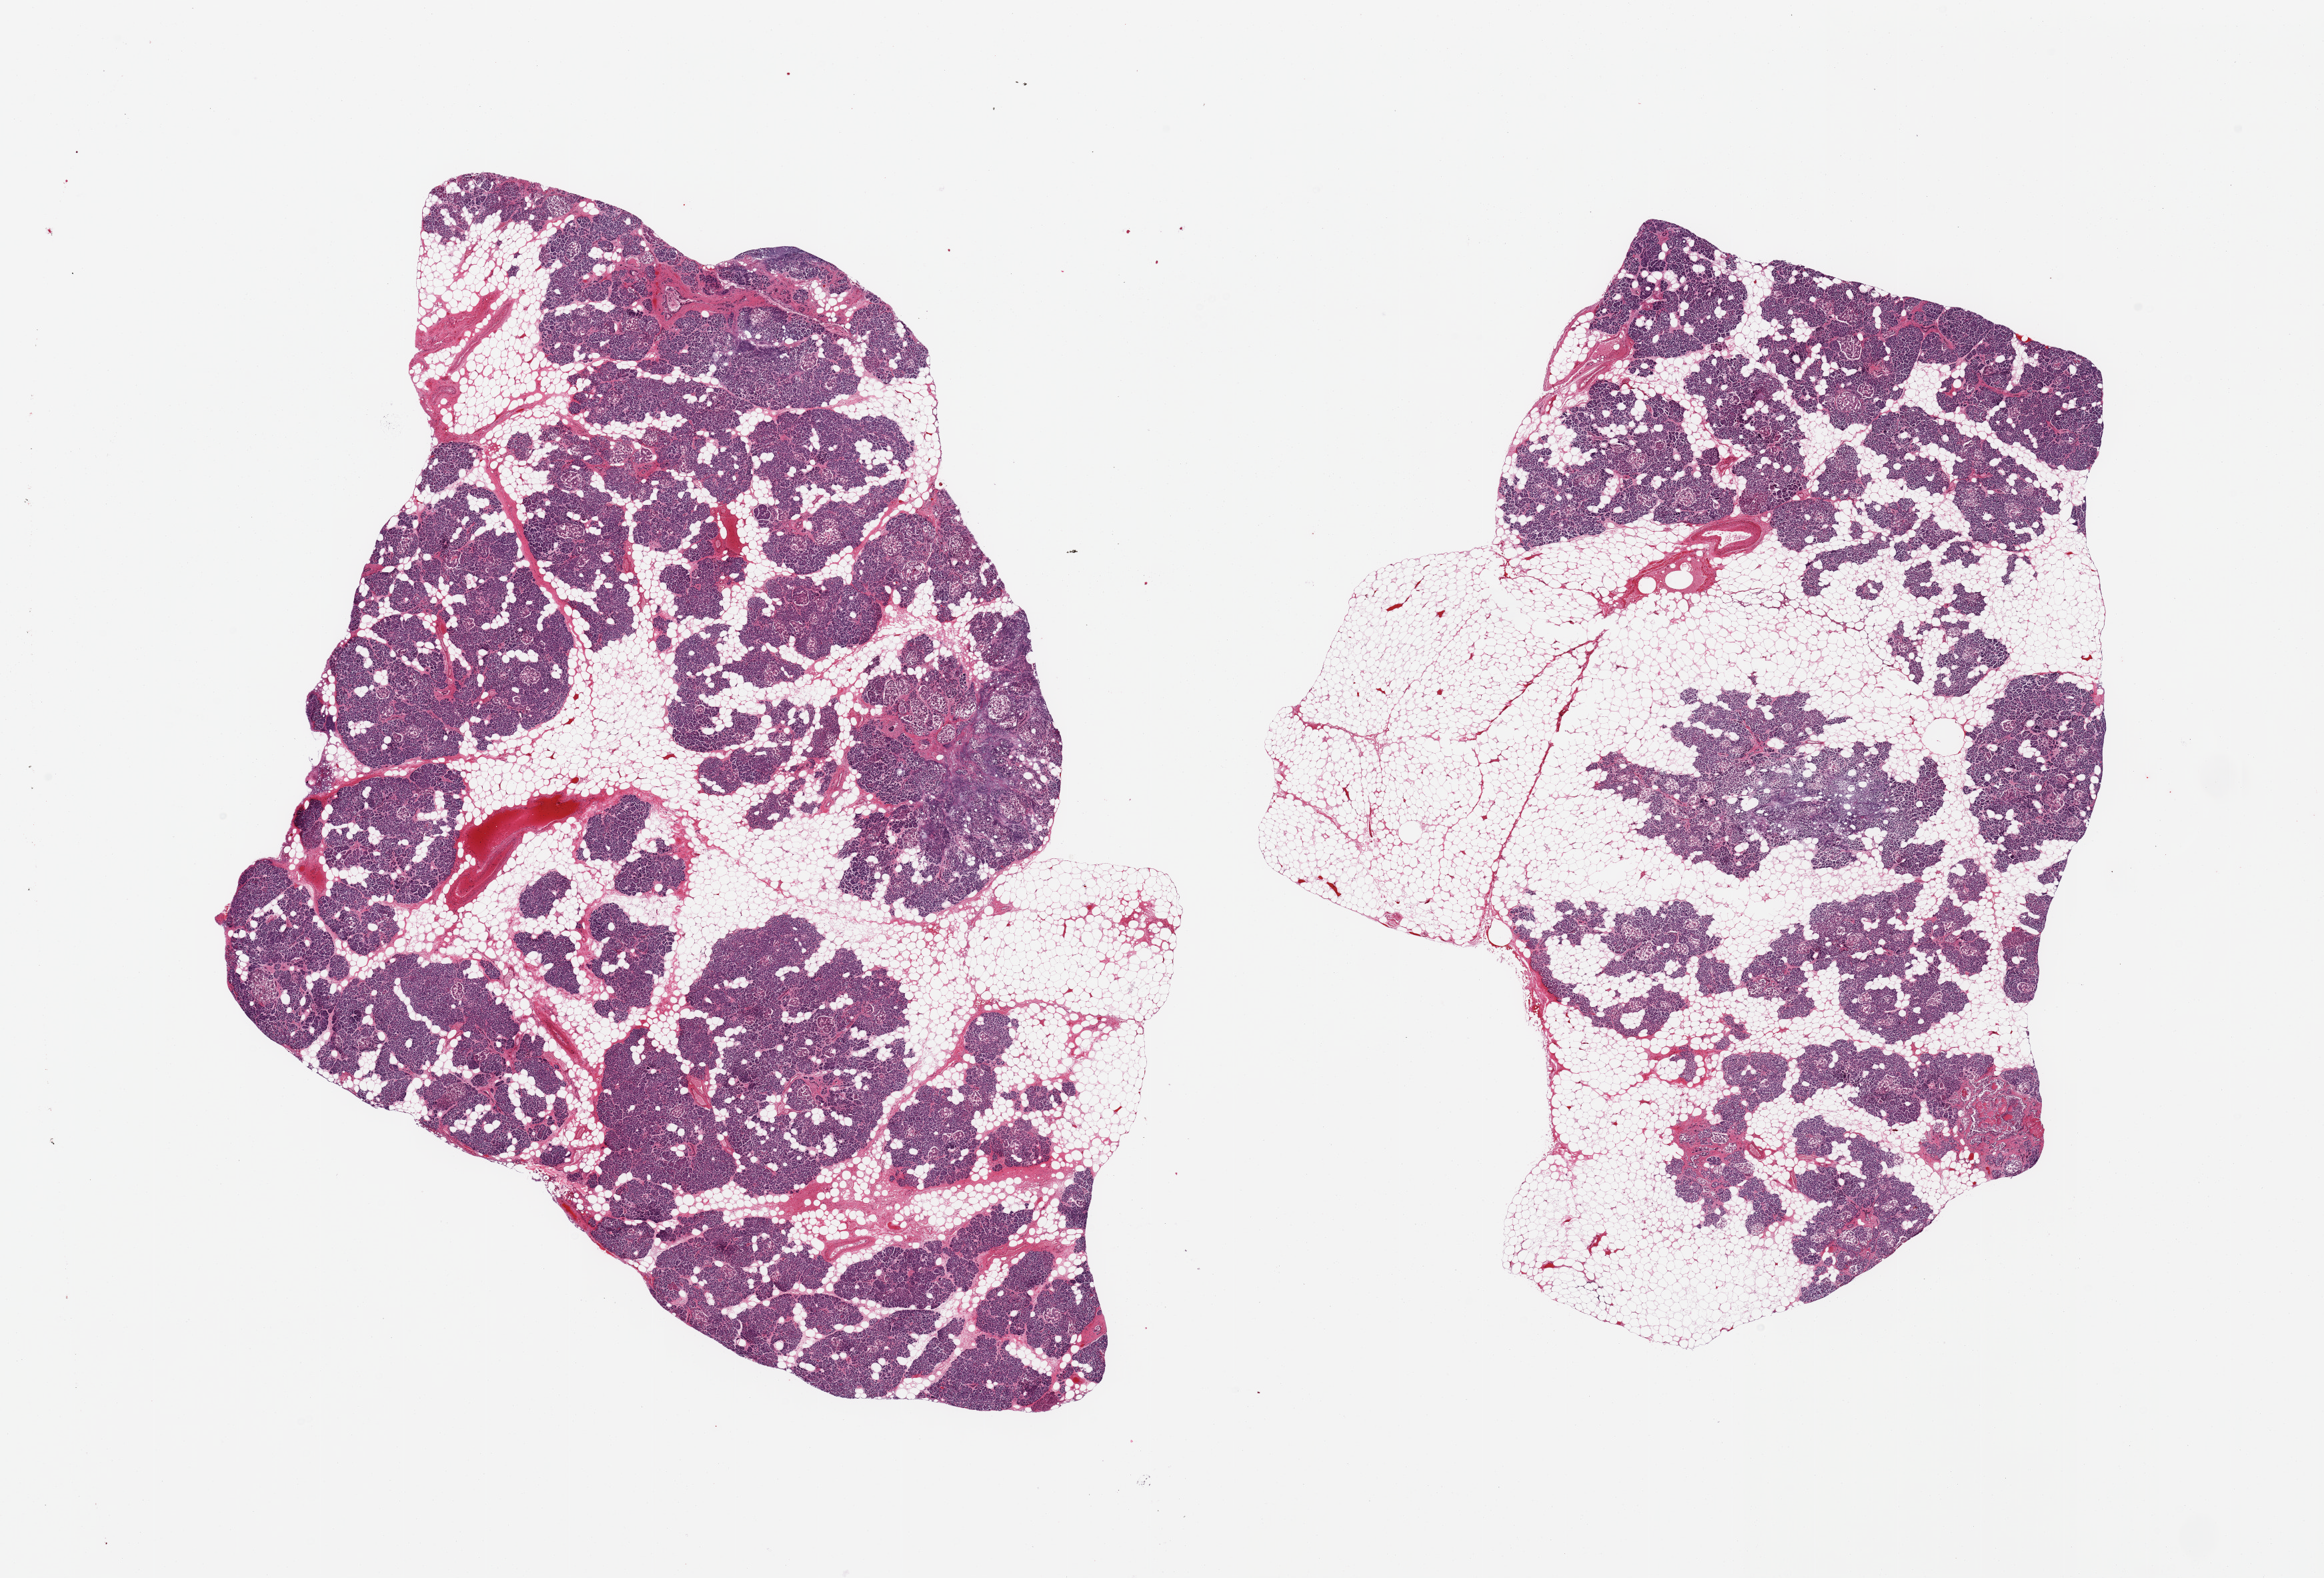
Whole-slide image, haematoxylin and eosin stain — shown as a low-resolution overview of the whole scanned area (about 27.6 x 18.7 mm); PAXgene-fixed, paraffin-embedded tissue; target tissue: pancreas; donor tissue sample. Donor: male.
Review note (as recorded): 2 pieces, moderate interstitial fat; moderate saponification; Rare islets still visible but degenerating.